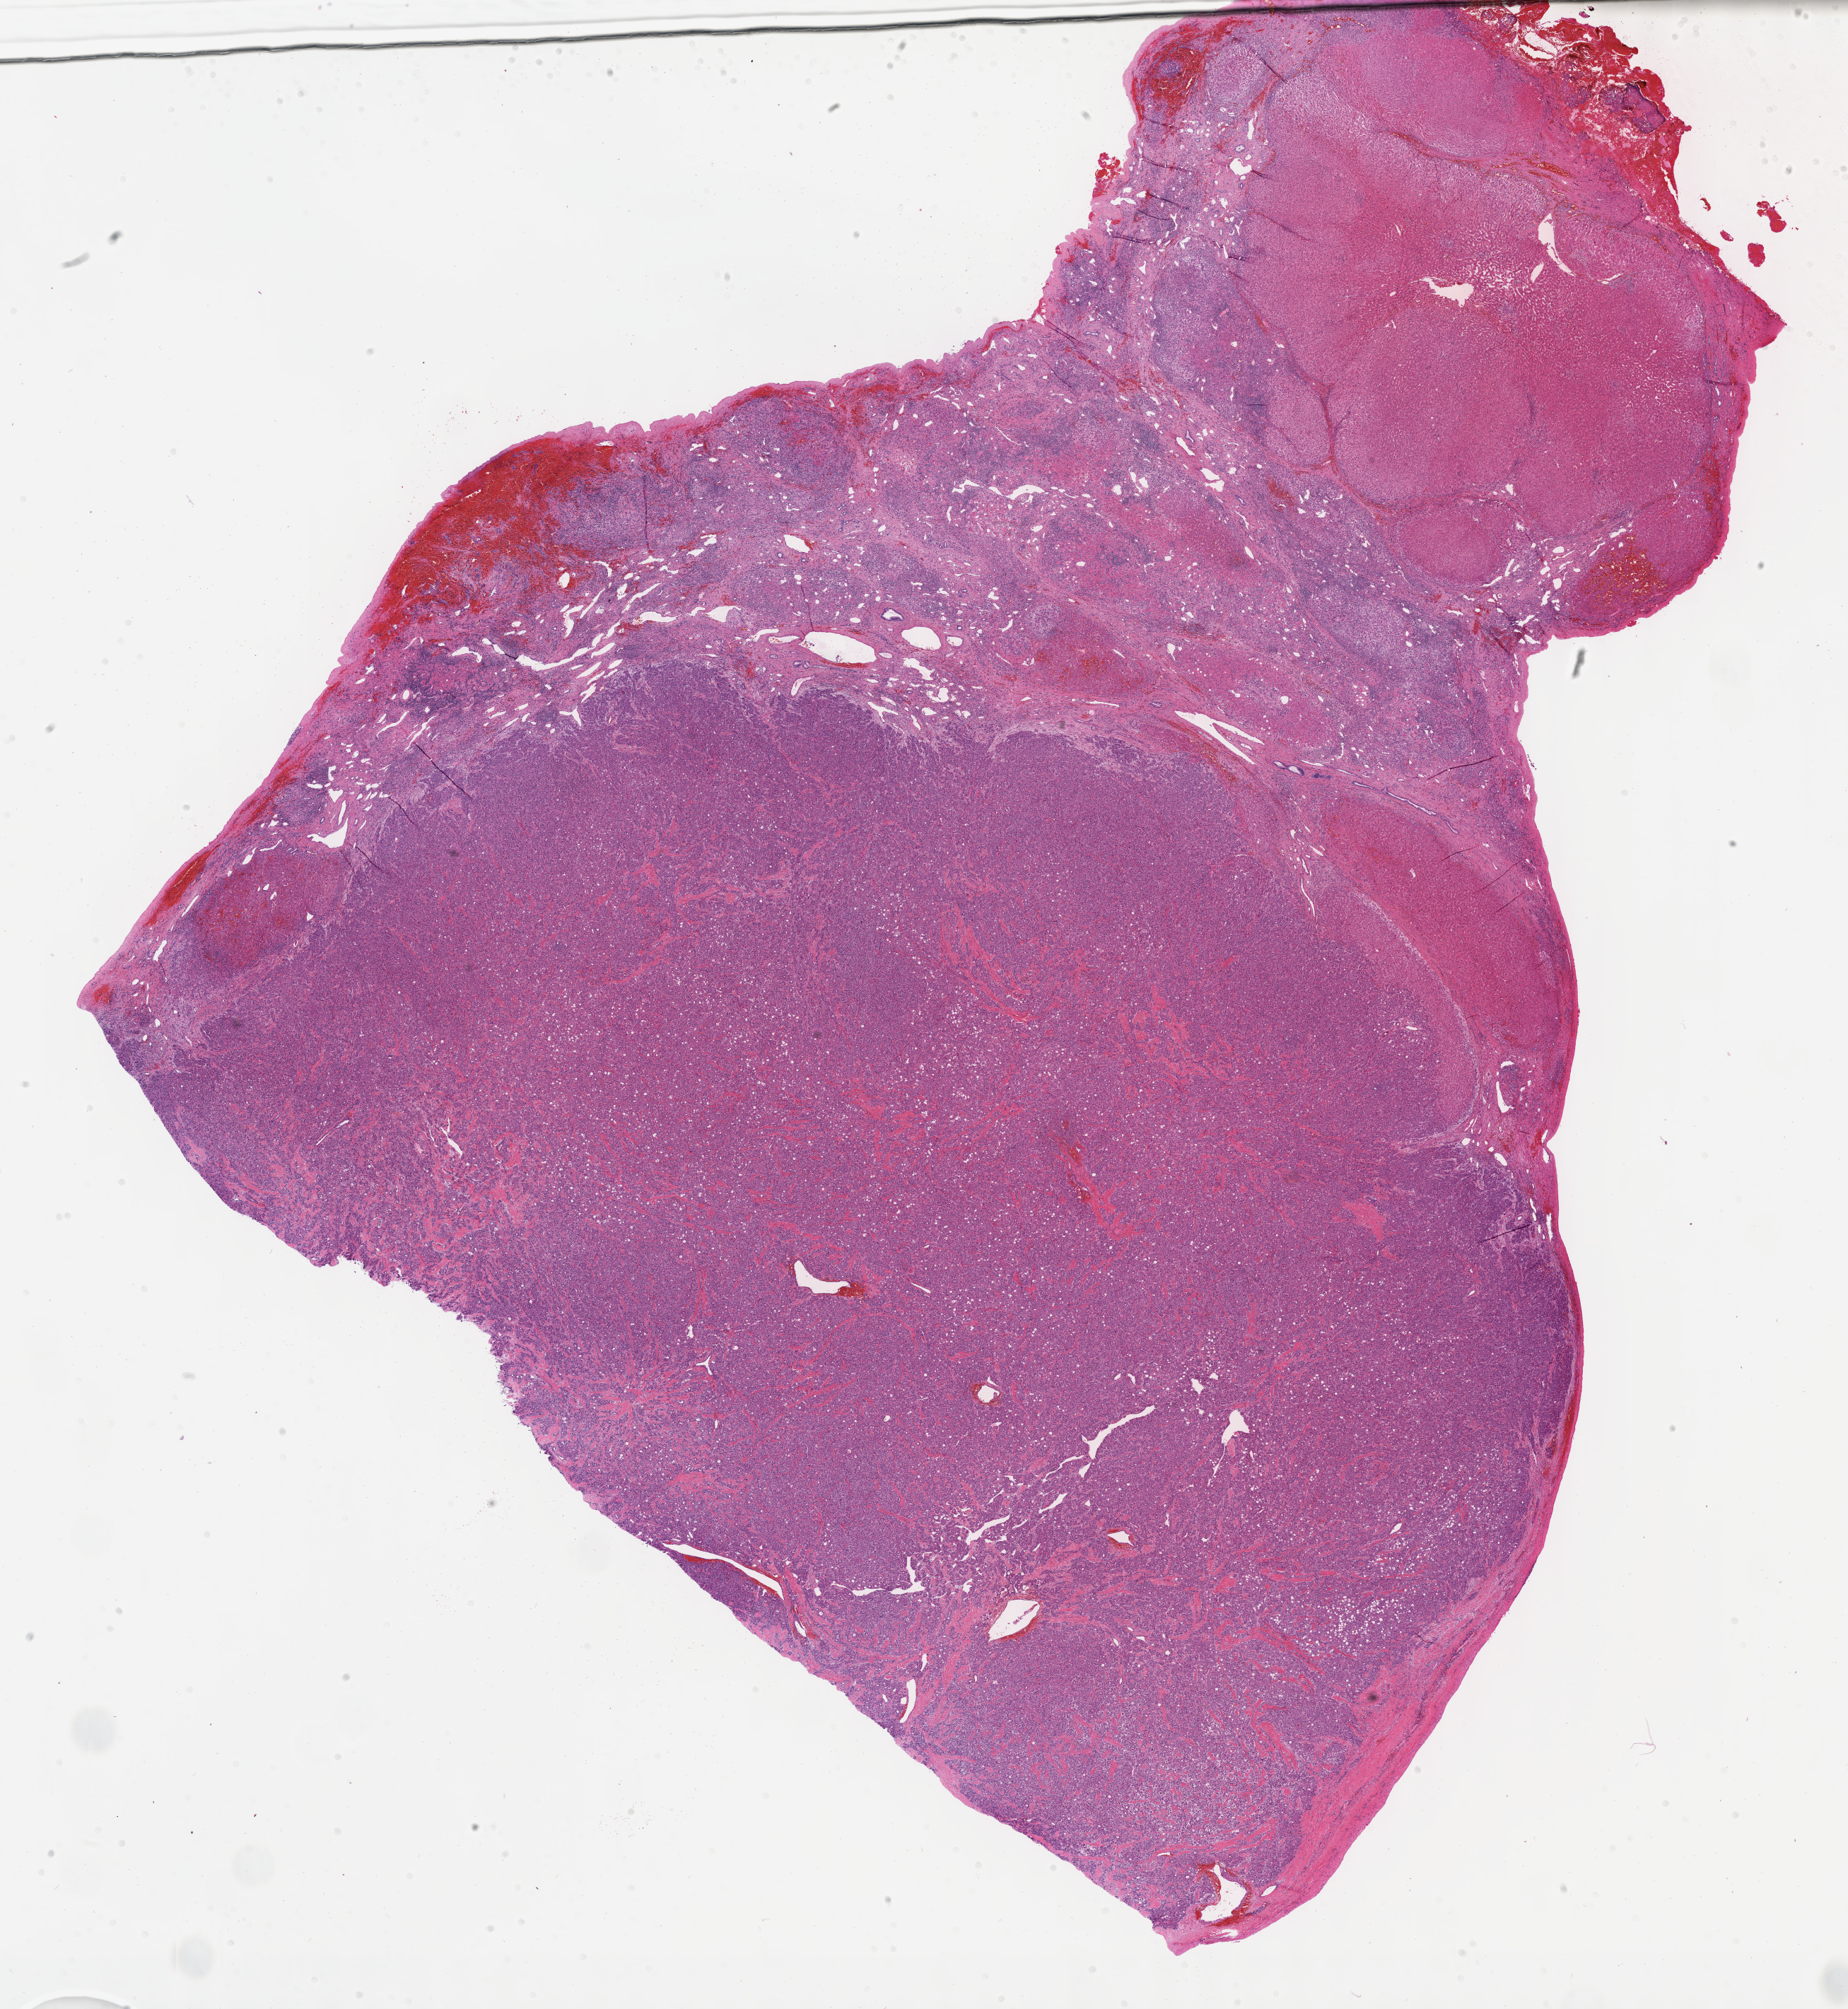
Digitized Hematoxylin and eosin (H&E) stained tissue section (whole slide) — whole scanned area (about 21.1 x 23.0 mm, slide scanned at 40x) shown as a low-resolution overview; FFPE section; sample: primary tumour, liver. Male, age 62 years at initial diagnosis. Histologic grade: G2 (moderately differentiated).
- histologic diagnosis: Hepatocellular carcinoma, NOS
- AJCC pathologic stage: II